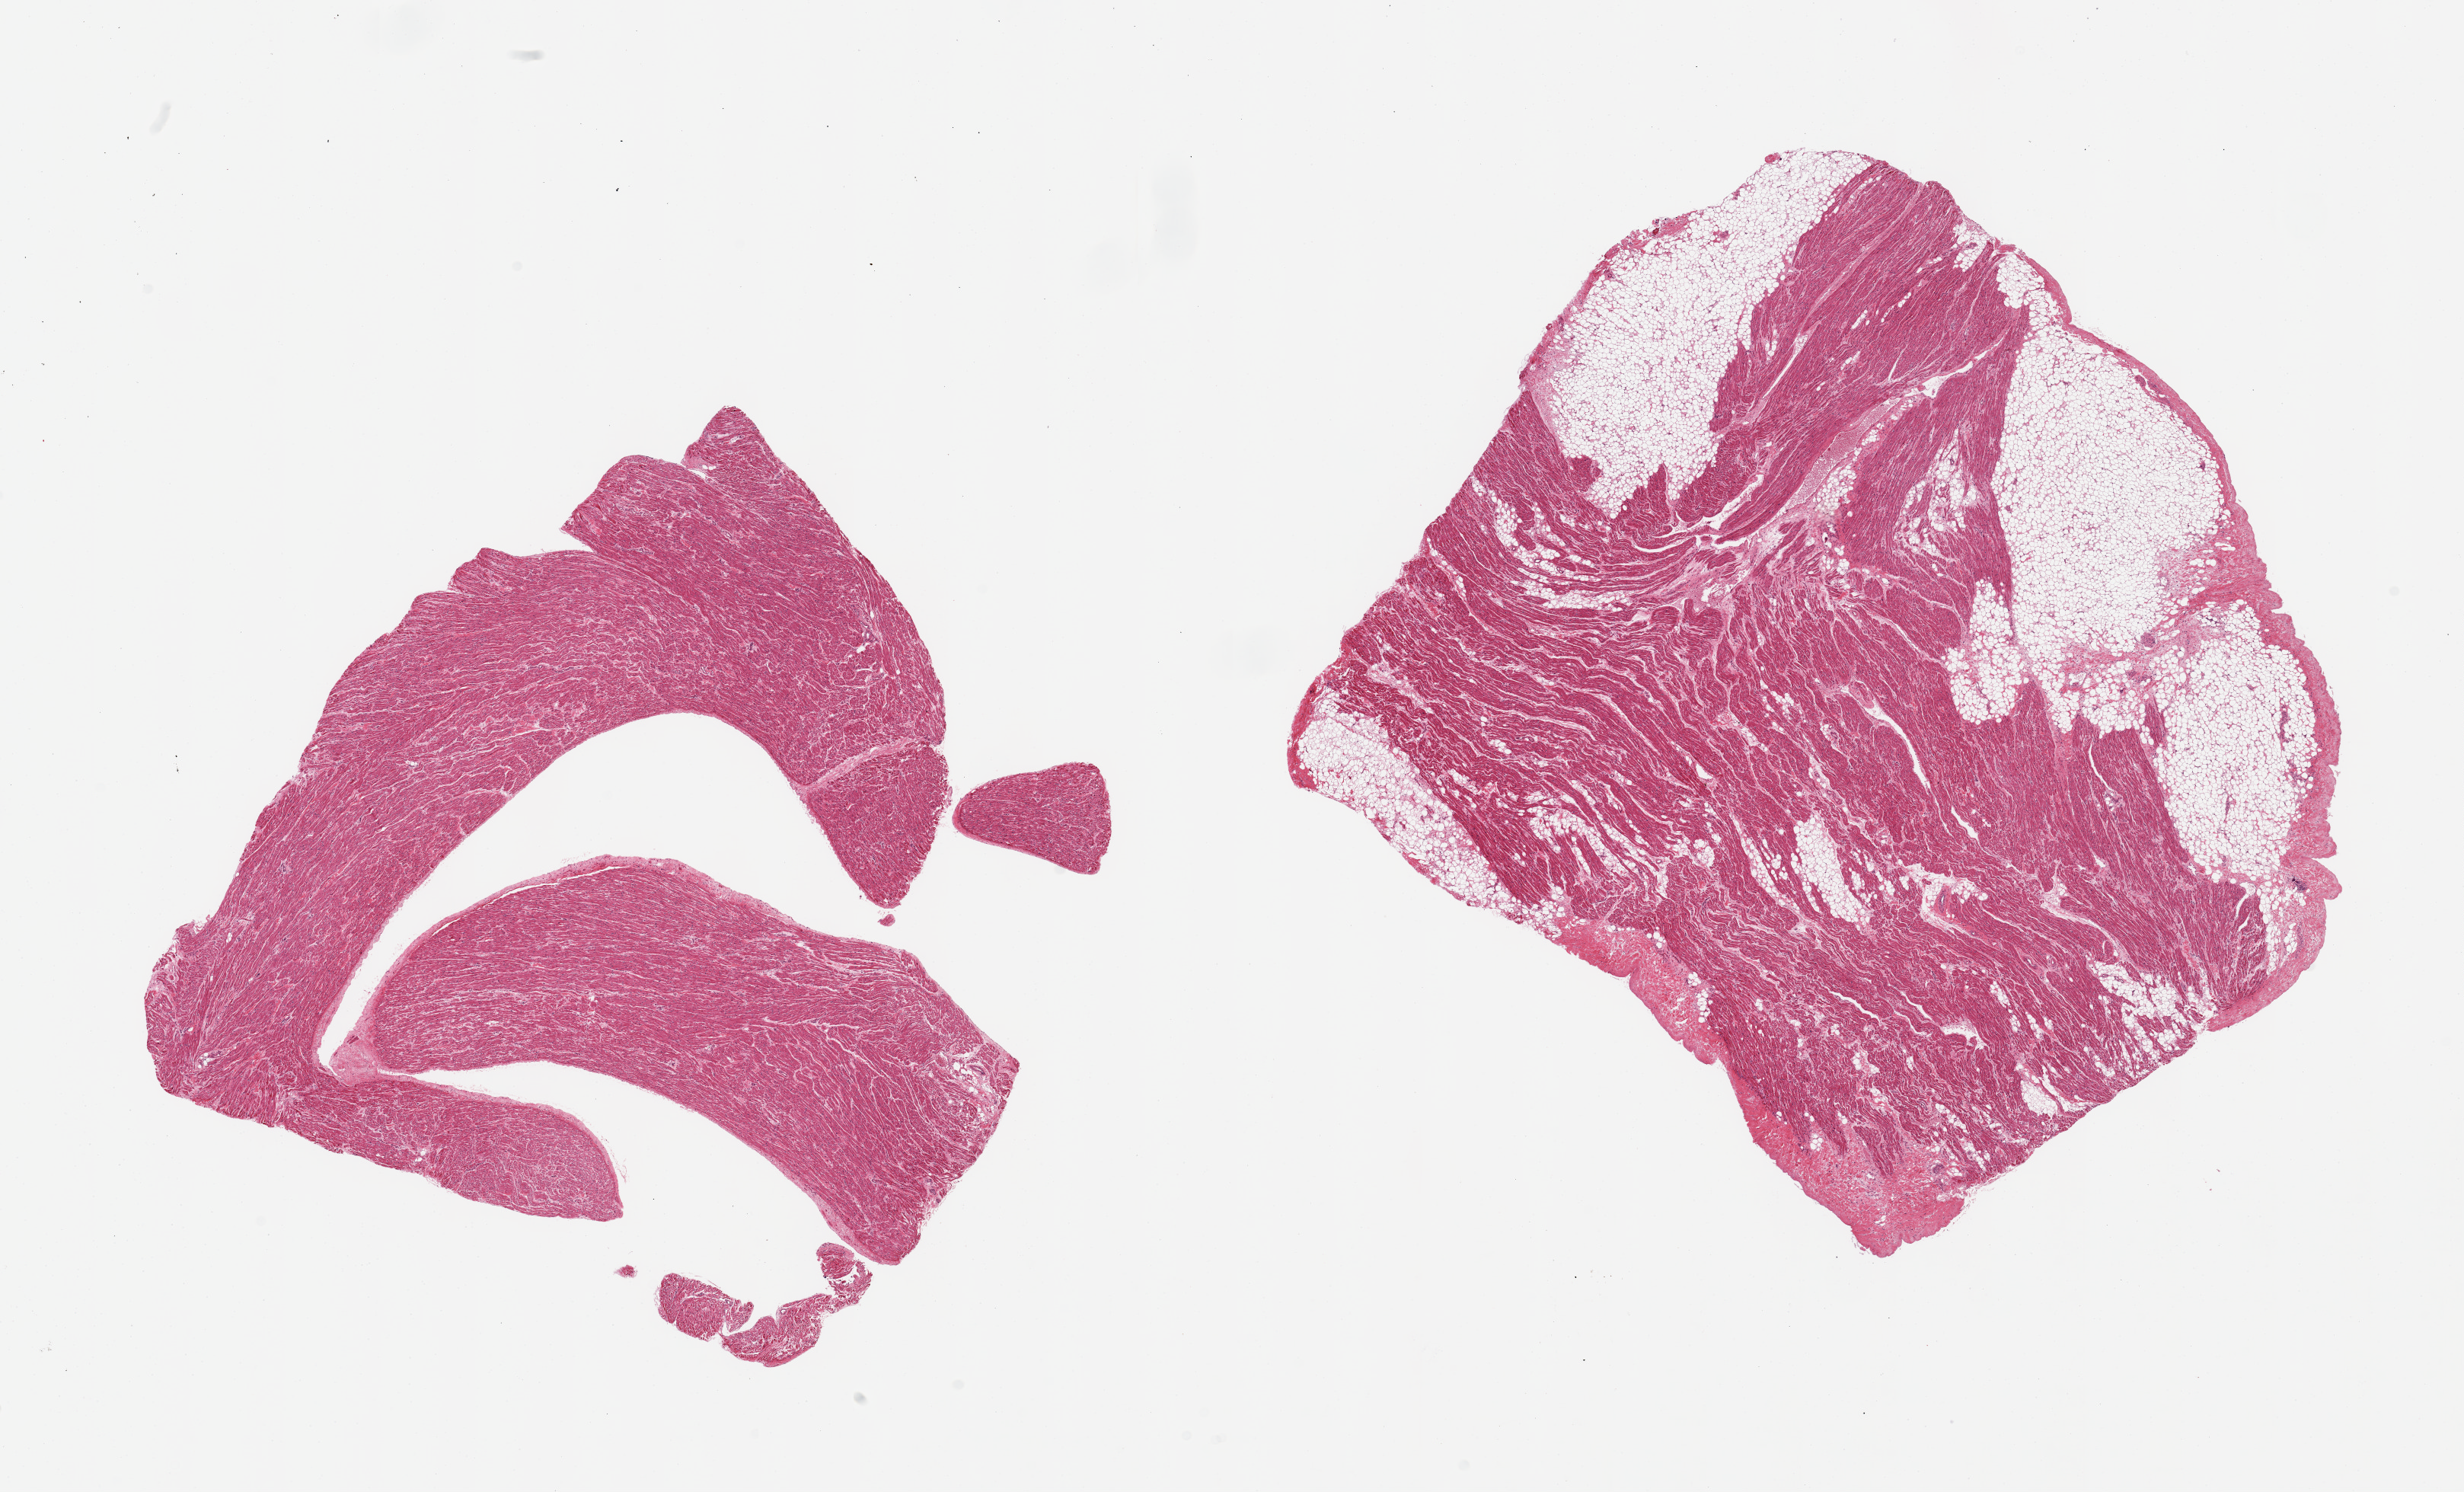
Digitized H&E-stained section, brightfield — a low-resolution overview of the entire scanned area, about 25.6 x 15.5 mm (acquisition: 20x scan); PAXgene-fixed, paraffin-embedded tissue; section of auricular appendage (target tissue); donor tissue sample. Donor: female.
Pathologist's review note for this sample: 2 pieces, no abnormalties.